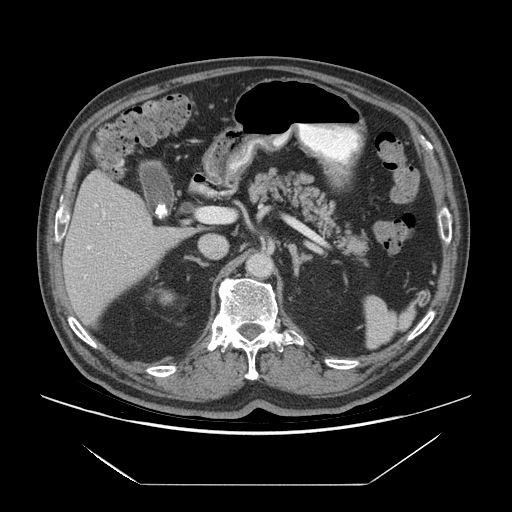
Contrast-enhanced abdominal CT (liver protocol), one axial slice. Position 34 of 75 along the scan axis. Reconstruction kernel STANDARD. Soft-tissue window (W 400 / L 40 HU). 2.5 mm slice thickness. 512 × 512 image matrix, field of view 420 × 420 mm. From the clinical record (not read from this slice): diagnosis: hepatocellular carcinoma (patient treated with transarterial chemoembolisation; whether this scan precedes or follows treatment is not stated here); TNM stage (as recorded): Stage-I; Child-Pugh class: A; tumour differentiation: well differentiated; tumour nodularity: uninodular.
Outlined on this slice (semi-automatically segmented with operator editing):
- liver parenchyma outside the tumour (the mass and vessels are separate outlines, so this box may not span the whole liver): bounding box [x1, y1, x2, y2] px = [62, 170, 192, 324]
- liver vessels: [84, 204, 105, 278]